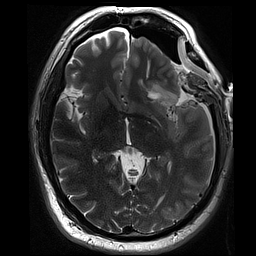
Brain MRI from a brain-tumour surgery series, one axial slice; position 46 of 70 along the scan axis; 2 mm slice thickness; 256 × 256 image matrix, field of view 220 × 220 mm. Case-level facts recorded for this patient, not image findings: histopathology: Oligodendroglioma; WHO grade: 3; IDH mutation: yes.
Outlined on this slice (manually delineated by an expert):
- residual tumour: box from (x=152, y=85) to (x=178, y=107) px